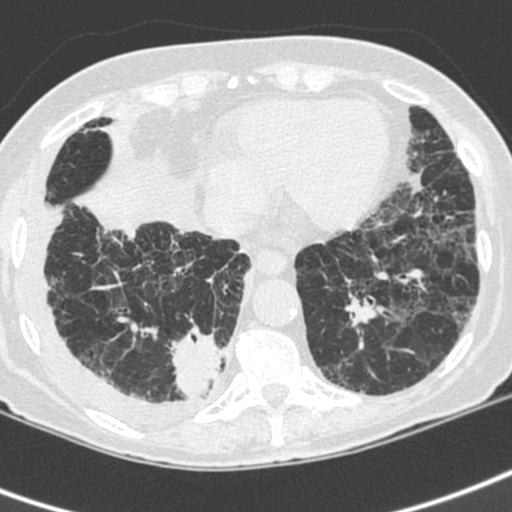
Axial slice from a low-dose chest CT screening exam, first (baseline) screen, lung window (W 1500 / L -600 HU), standard (soft-tissue) reconstruction kernel (C), 120 kVp, slice 138 of 192 in the series, 512 × 512 image matrix. Female, age 73 years at enrolment. Current smoker at enrolment.
Expert reader's lesion annotation, bounding box [x1, y1, x2, y2] px = [156, 318, 235, 406]. The exam's reader record, not a measurement of the box and not confirmed to be the same lesion: non-calcified nodule or mass ≥4 mm, right lower lobe, 35 × 30 mm, spiculated (stellate) margins, soft tissue attenuation.